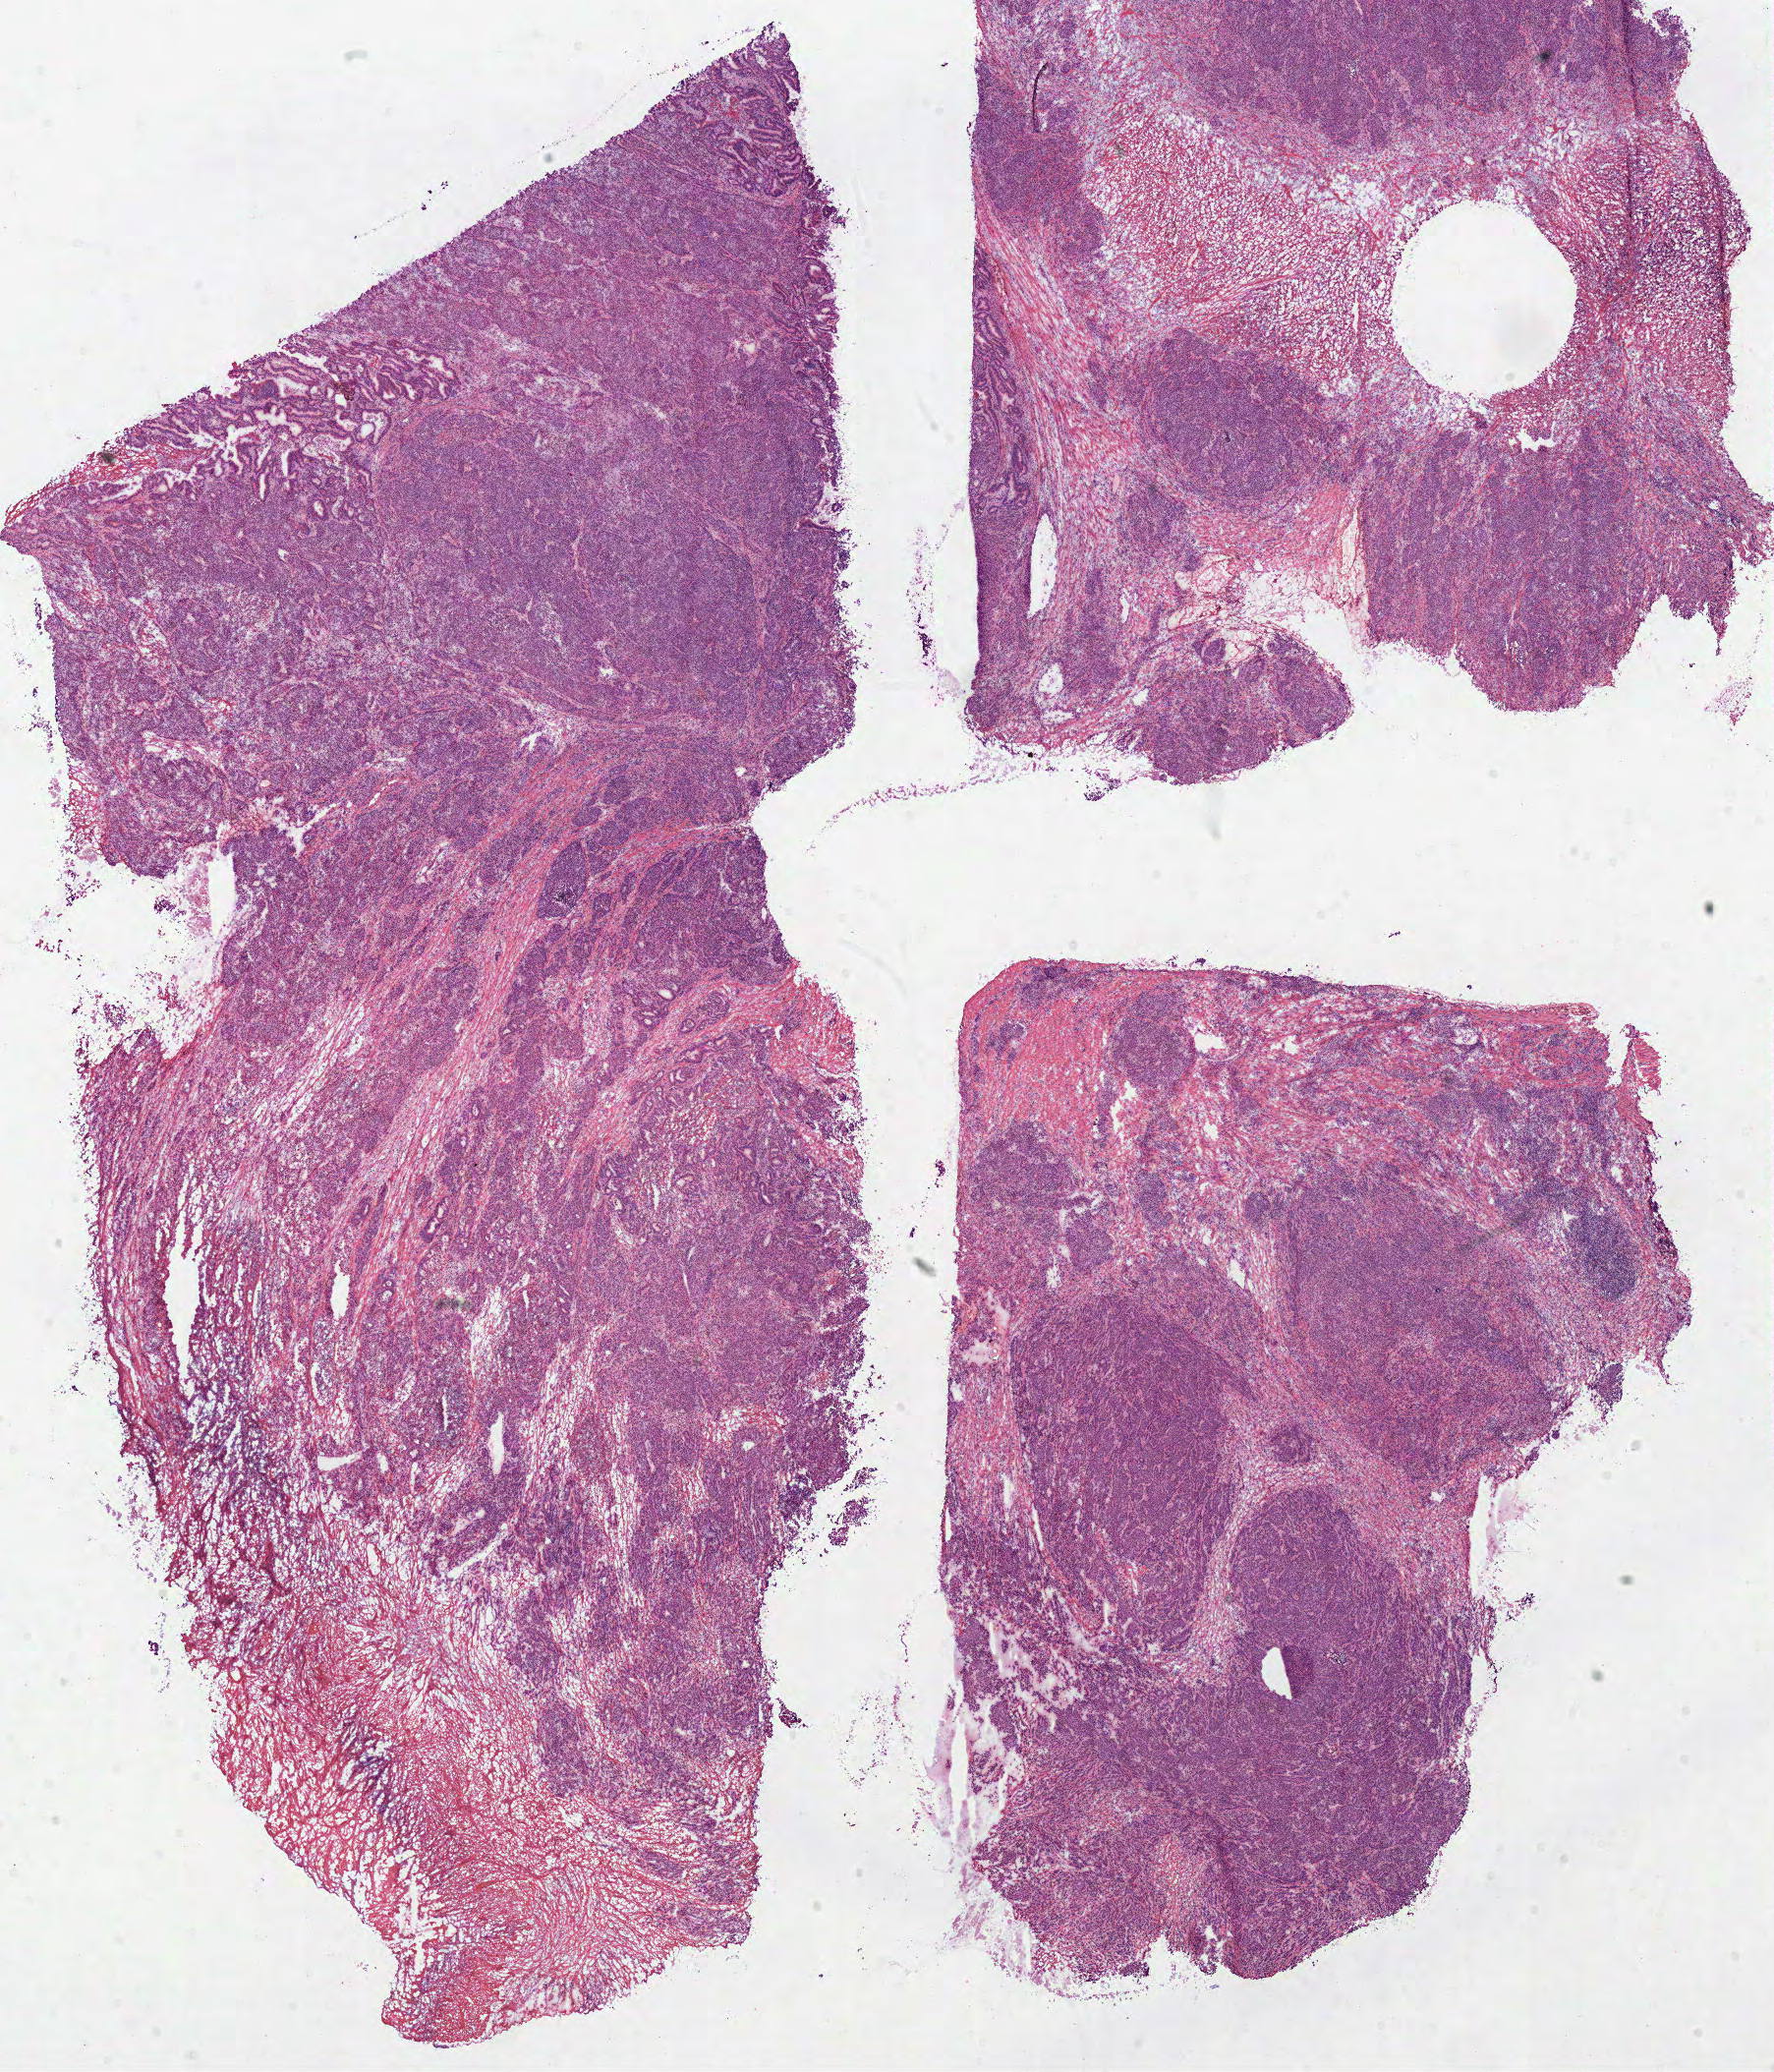
Digitized H&E-stained tissue section (whole slide), shown as a low-resolution overview of the whole scanned area (about 14.2 x 16.6 mm); frozen section from the top of the tissue portion; primary tumour sample from the colon. Male patient; age at initial diagnosis 46 years. Pathologist review of this section (percent, as recorded): tumour cells 67%, tumour nuclei 75%, normal cells 8%, stromal cells 25%, necrosis 0%.
* histologic diagnosis: Adenocarcinoma, NOS
* AJCC pathologic stage: IIA (6th edition)